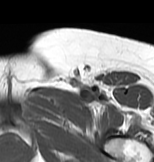
MRI of an extremity soft-tissue mass, one axial slice. MR volume resampled by the dataset authors to the PET/CT grid (not the native acquisition matrix). 154 × 162 image matrix, field of view 150 × 158 mm. Female patient. From the clinical record (not read from this slice): histological type: myxofibrosarcoma; grade: intermediate; site of the primary tumour: left thigh.
Outlined on this slice (expert contour drawn on MRI and transferred to this co-registered scan by the dataset authors):
- gross tumour volume including surrounding oedema: bounding box [x1, y1, x2, y2] px = [31, 86, 116, 115]